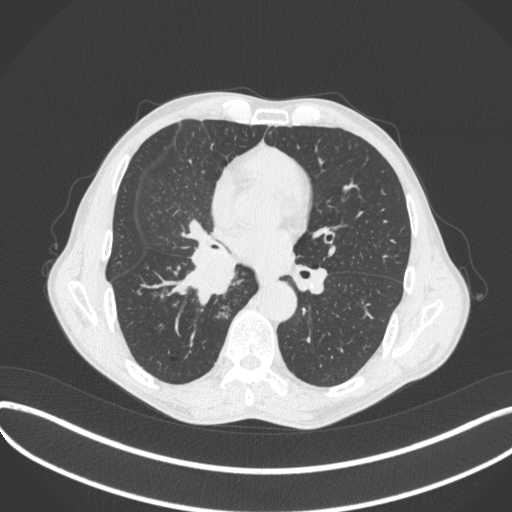
Chest CT, one axial slice. Slice 218 of 481 in the series (ordered by position). Lung window (W 1500 / L -600 HU). 512 × 512 image matrix, field of view 400 × 400 mm. Patient: male, 65 years. Case-level facts recorded for this patient, not image findings: clinical TNM (as recorded): T2a N0 M0; histopathological grade: G2.
Structures marked on this image (rectangle marked by the reading radiologist):
- lung tumour (recorded histology: squamous cell carcinoma): bounding box [x1, y1, x2, y2] px = [173, 236, 240, 309]